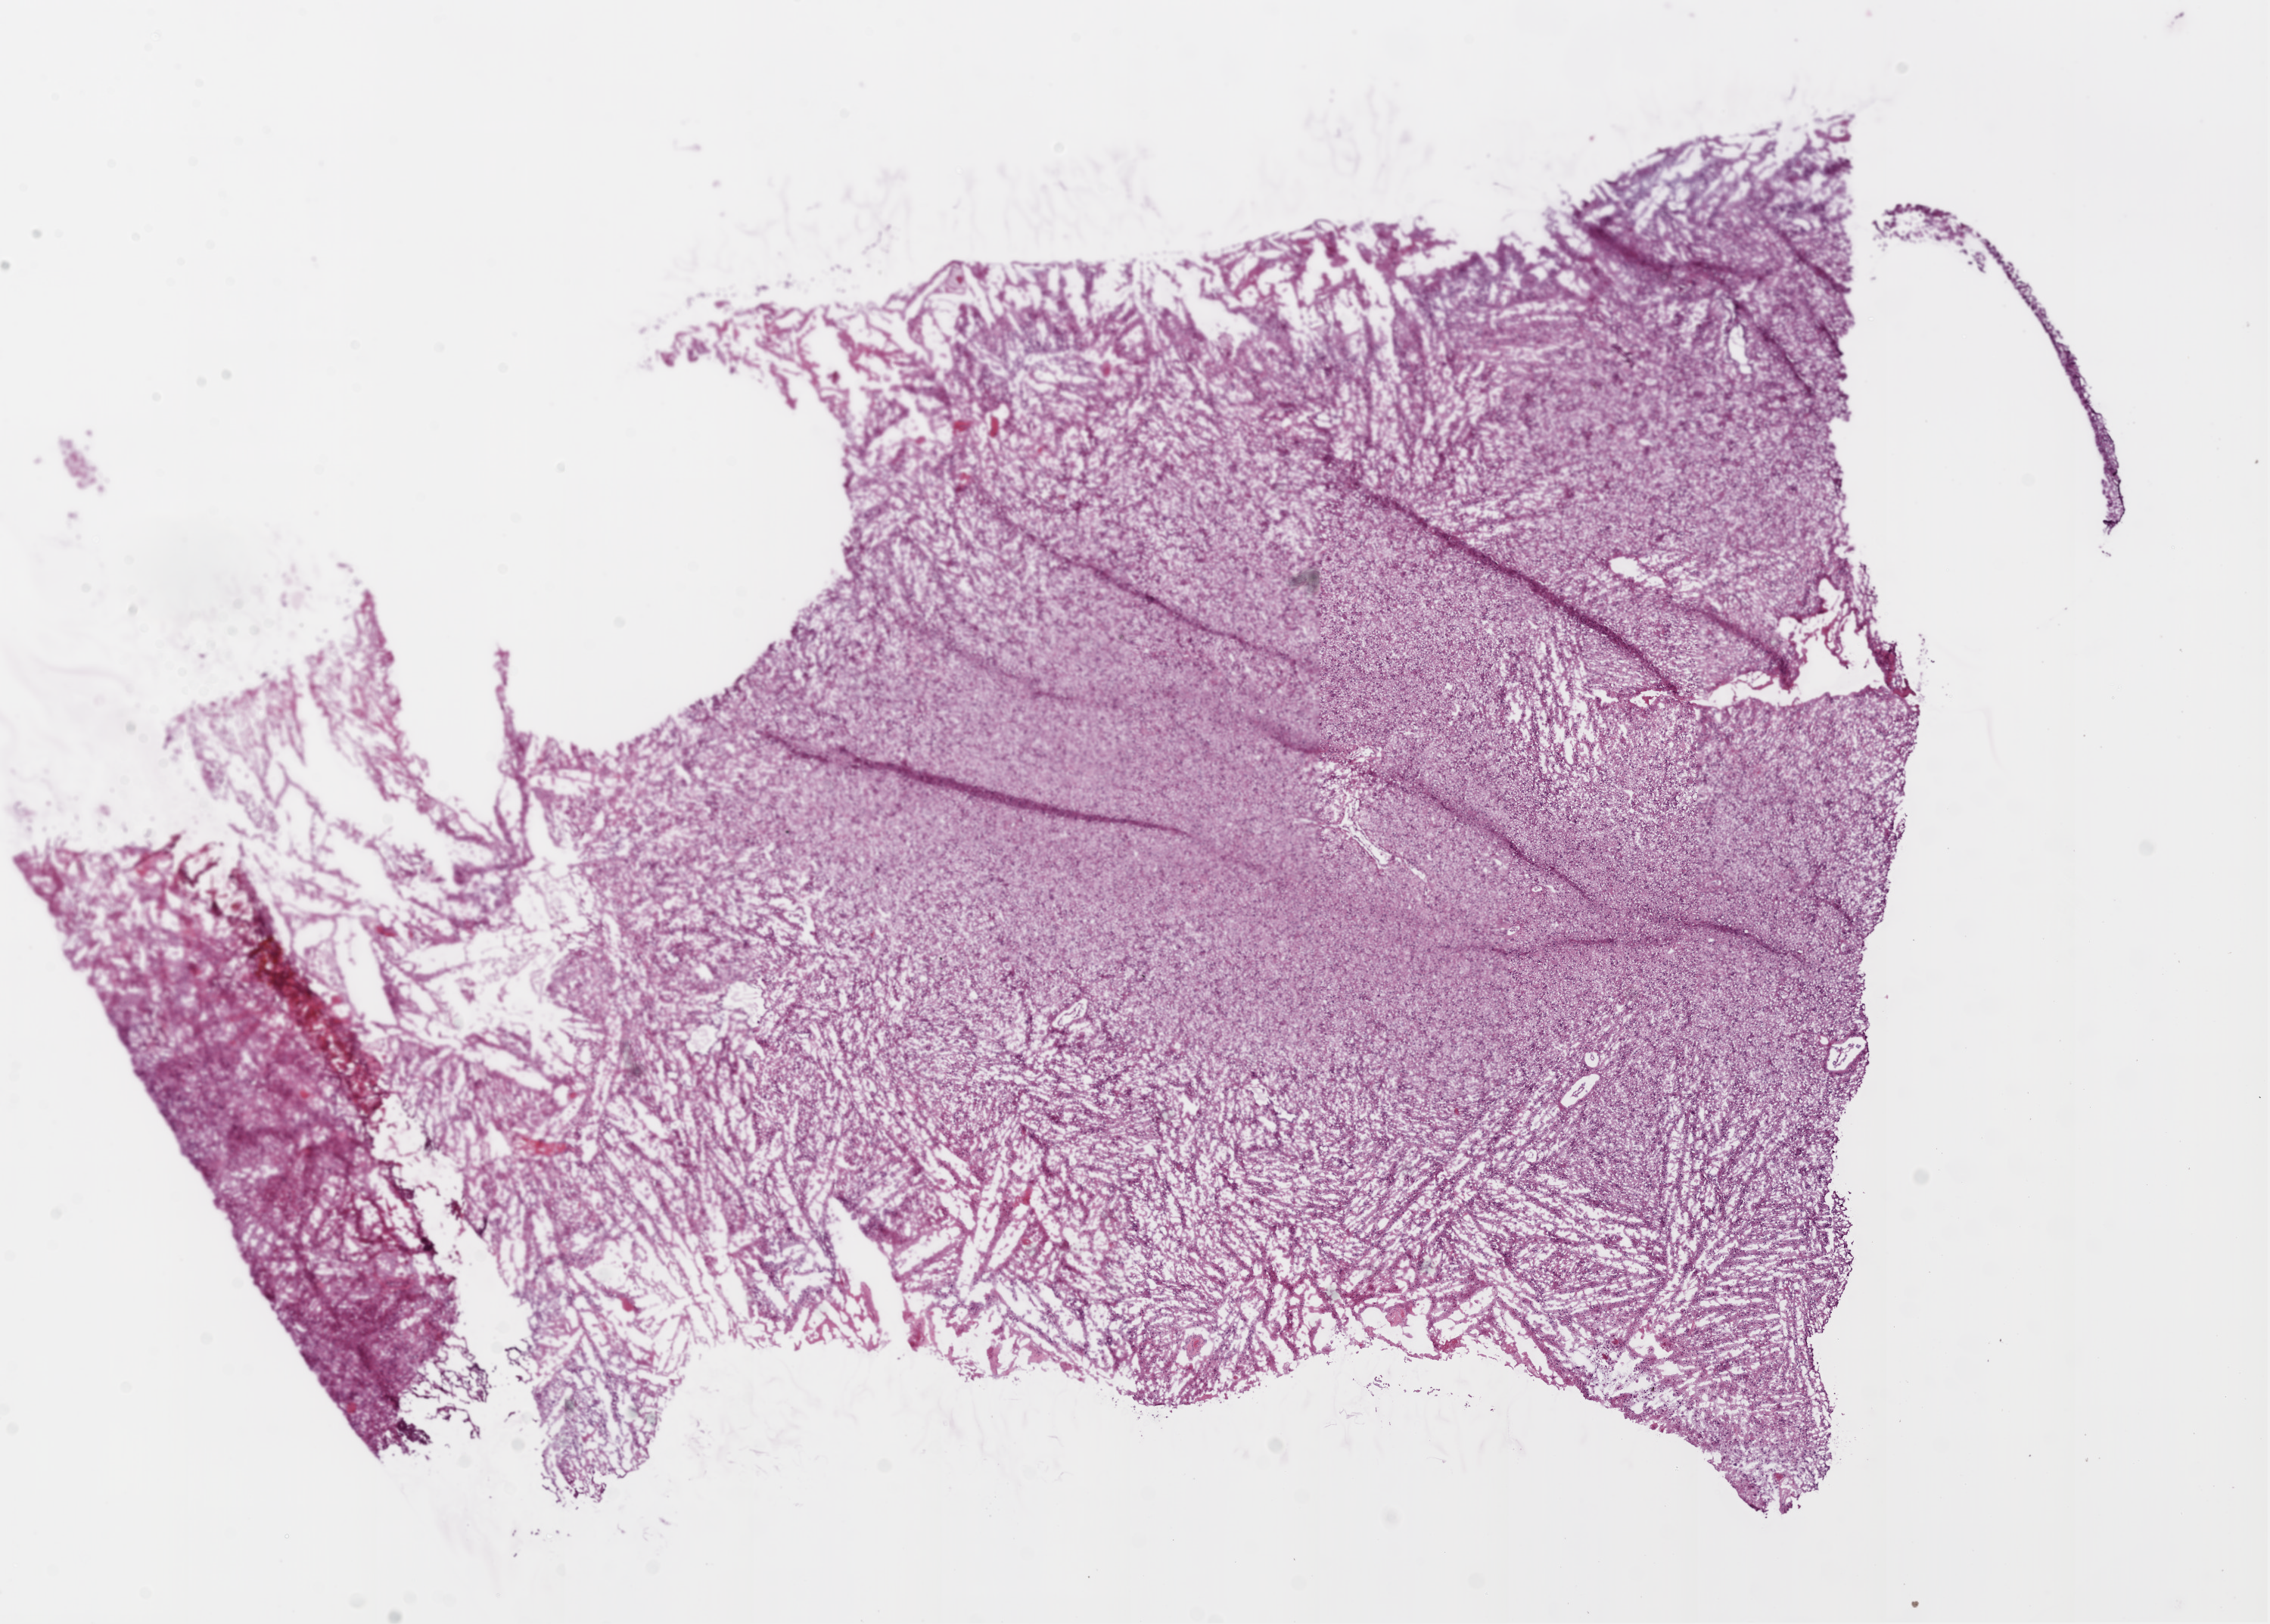
Digitized H&E-stained tissue section (whole slide), a low-resolution overview of the entire scanned area, about 12.0 x 8.6 mm (acquisition: 20x scan). Frozen section. Sample: primary tumour, brain. Male patient; age at initial diagnosis 68 years. Pathologist review of this section (percent, as recorded): tumour cells 100%, tumour nuclei 70%, normal cells 0%, stromal cells 0%, necrosis 0%.
Histologic diagnosis: Glioblastoma.